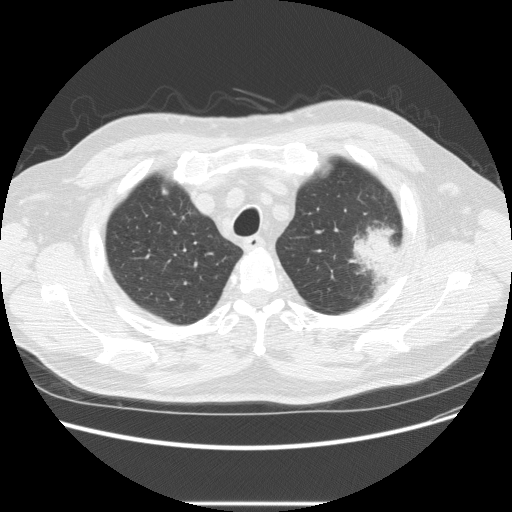
Low-dose screening chest CT, one axial slice. Position 189 of 233 along the scan axis. 120 kVp. Lung window (W 1500 / L -600 HU). 512 × 512 image matrix, field of view 380 × 380 mm.
Annotated regions visible in this slice (outlined manually by an expert reader):
- lesion 1 (tumor, upper lobe of left lung): bounding box <349,224,402,285> (left, top, right, bottom; pixels)